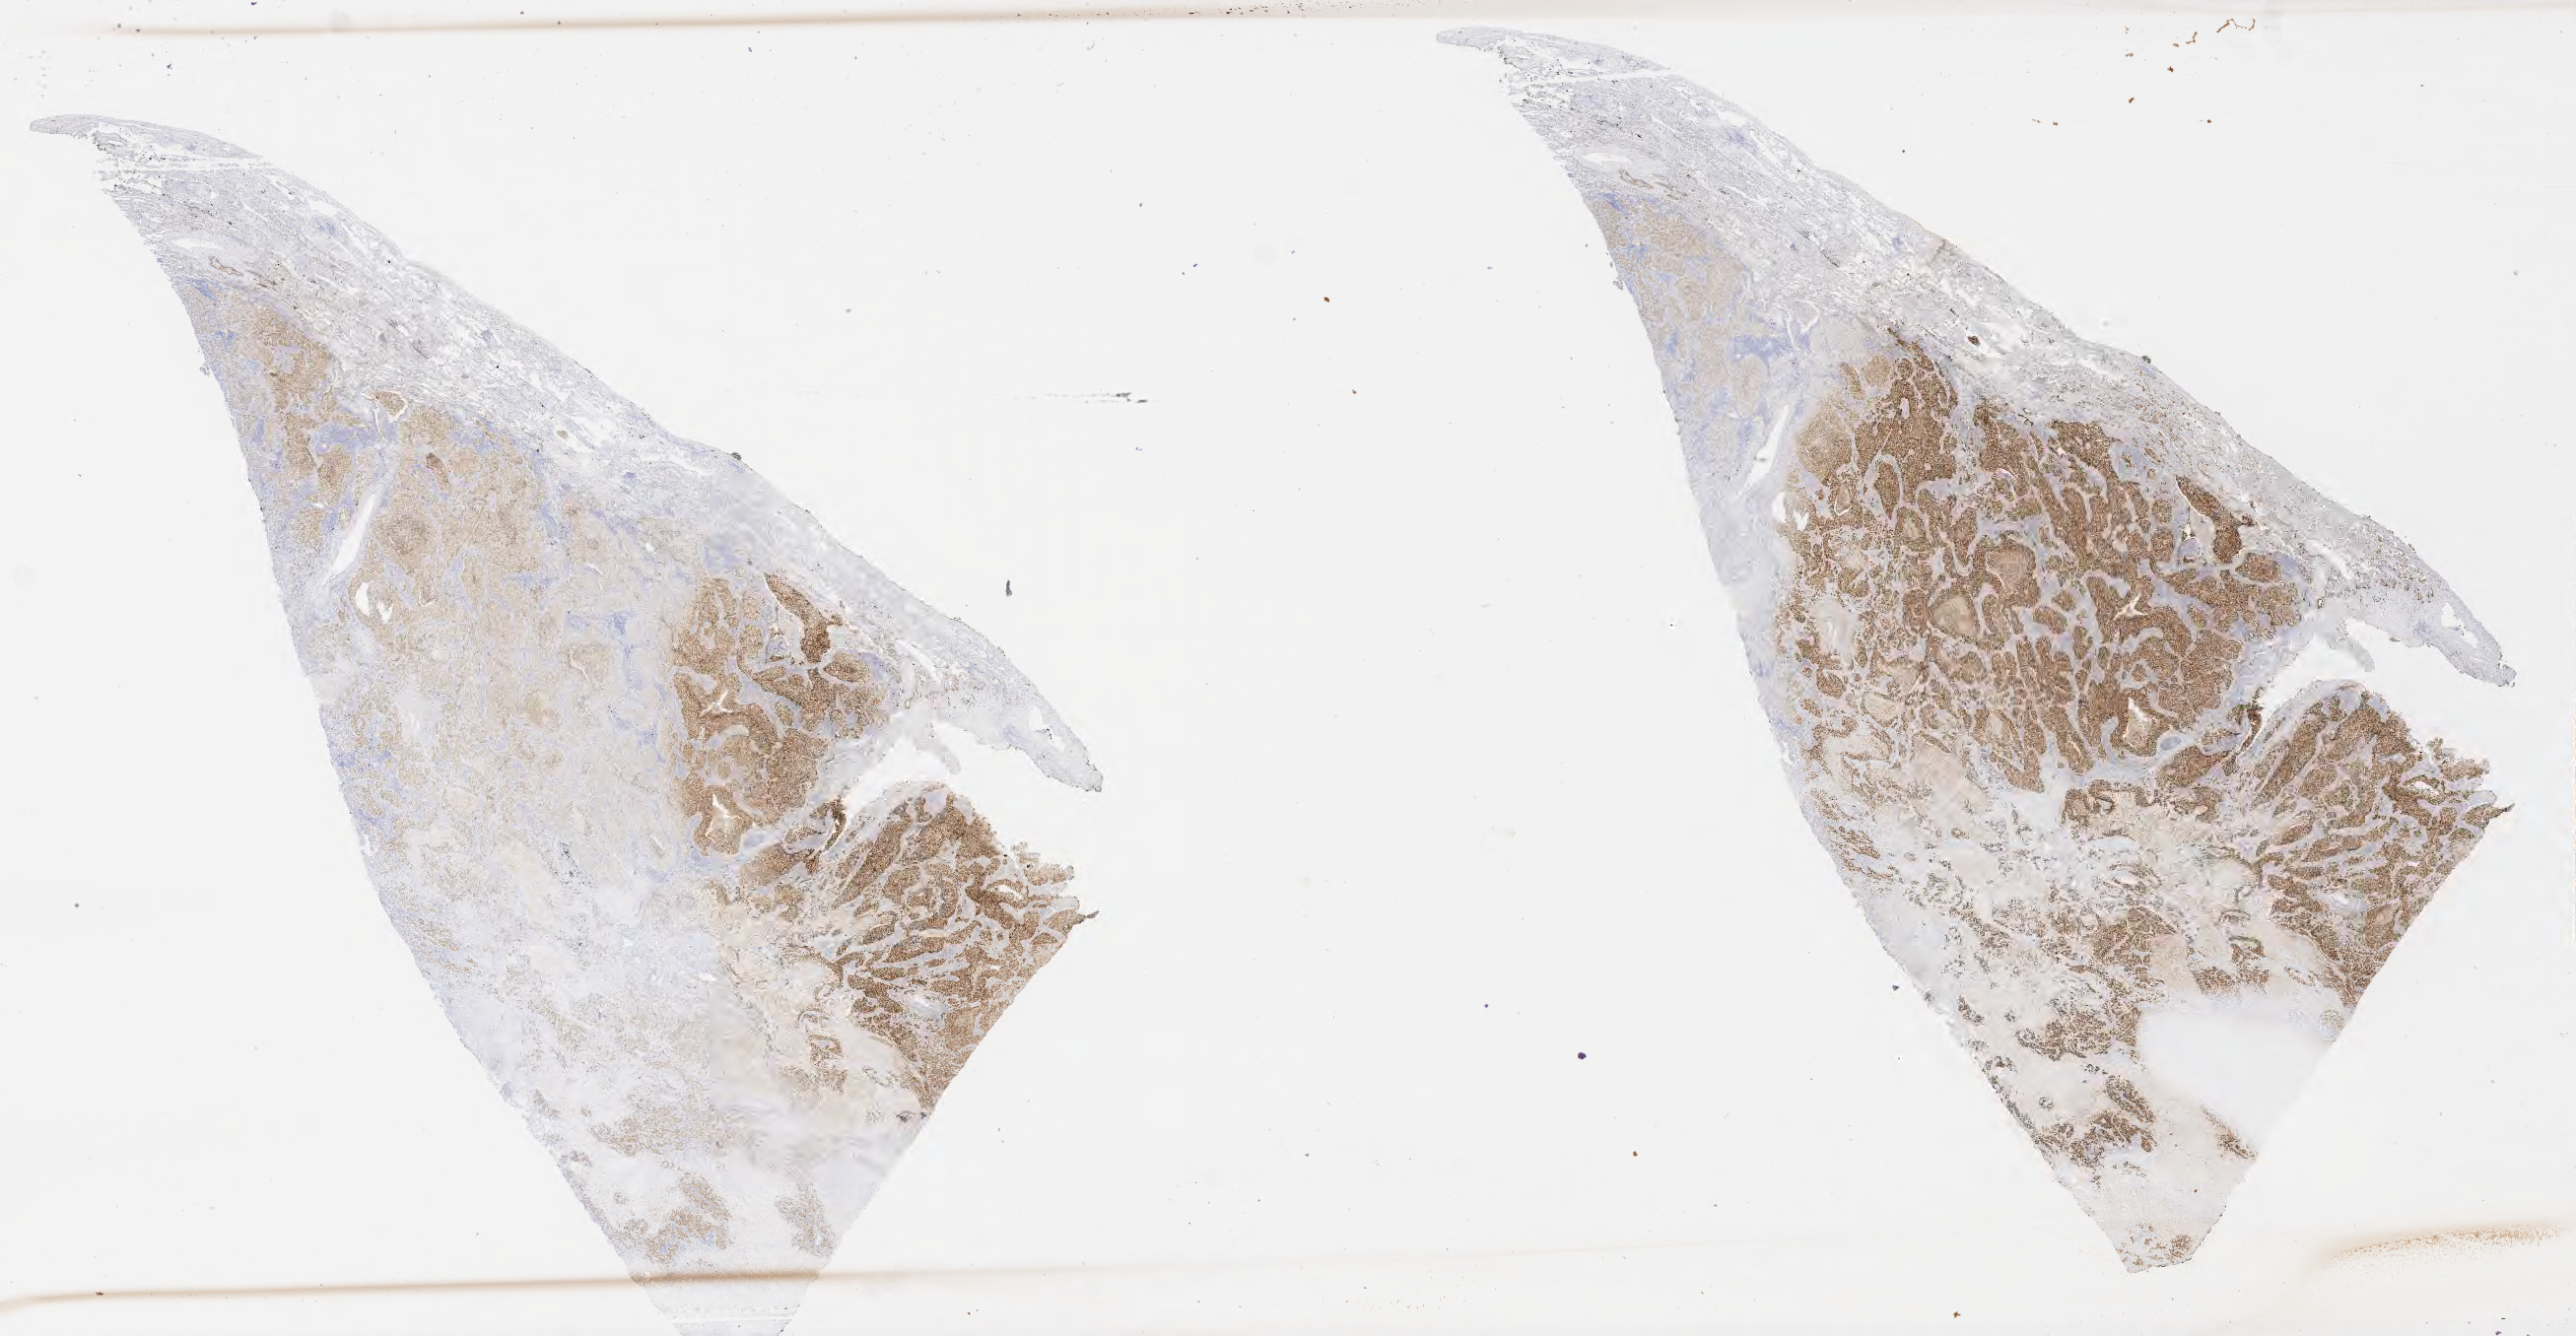
Whole-slide image, immunohistochemical stain for TTF-1 (thyroid transcription factor 1) — whole scanned area (about 42.3 x 21.9 mm) shown as a low-resolution overview, specimen: tumor tissue, site: lung (left). Patient: female, aged 69.
Histologic diagnosis: Squamous cell carcinoma, NOS.